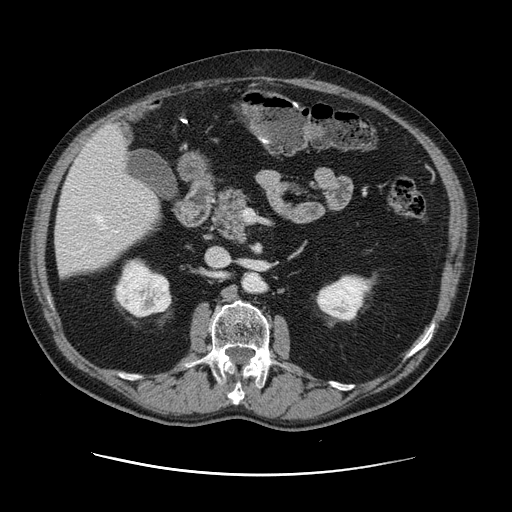
Contrast-enhanced abdominal CT, one axial slice; slice 57 of 141 in the series (ordered by position); soft-tissue window (W 400 / L 40 HU); 512 × 512 image matrix. Male patient, age 72 years. From the clinical record (not read from this slice): diagnosis: colorectal cancer liver metastases, imaged before liver resection; multiple liver metastases: yes; largest metastasis: 5.4 cm.
Structures marked on this image (expert manual segmentation):
- hepatic veins: bounding box (x1, y1, x2, y2) in pixels: (95, 215, 106, 230)
- liver: (56, 127, 161, 275)
- planned liver remnant (the part of the liver to remain after resection): (56, 182, 161, 276)
- portal vein (with intrahepatic branches): (100, 223, 103, 227)